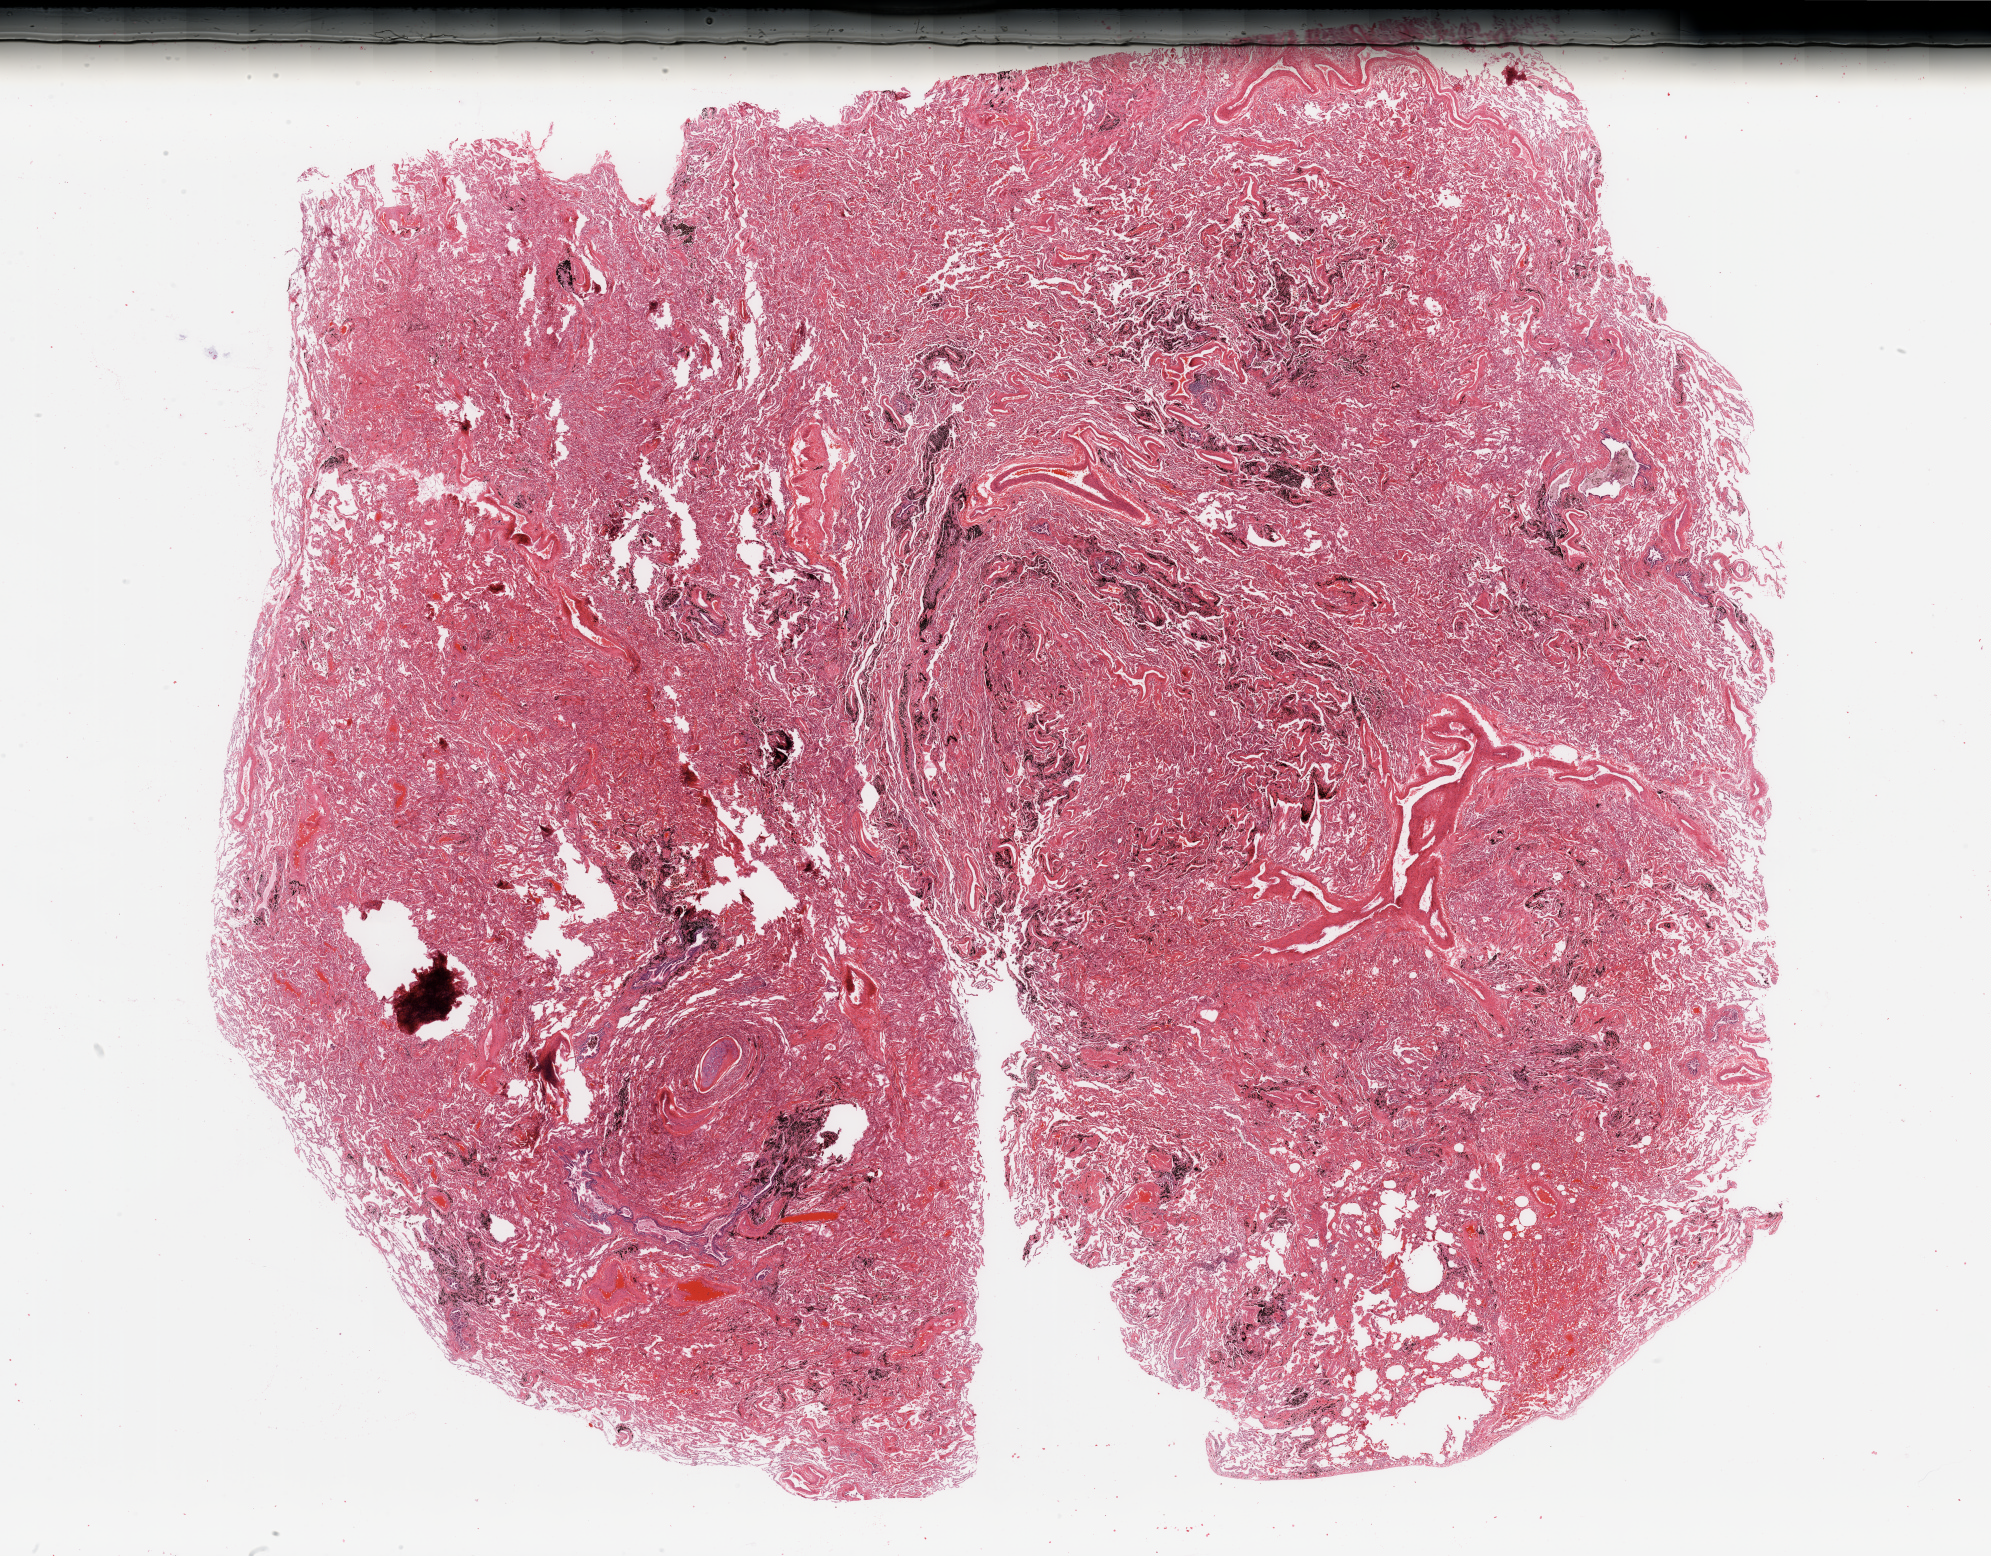
Whole-slide histology image, H&E-stained, shown as a low-resolution overview of the whole scanned area (about 31.5 x 24.6 mm, acquisition: 20x scan), normal (non-tumour) tissue sample, sampled site: lung. Male, 76 y/o.
This section: normal (non-tumour) tissue from the same patient. Patient diagnosis: Adenocarcinoma, NOS.